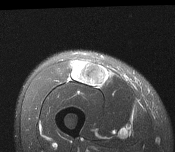
MRI of an extremity soft-tissue mass, one axial slice. Position 54 of 116 along the scan axis. T2-weighted fat-saturated. MR volume resampled by the dataset authors to the PET/CT grid (not the native acquisition matrix). 3.27 mm slice thickness. 175 × 152 image matrix, field of view 171 × 148 mm. Male patient. From the clinical record (not read from this slice): histological type: pleiomorphic leiomyosarcoma; grade: intermediate; site of the primary tumour: right thigh.
Outlined on this slice (expert contour drawn on MRI and transferred to this co-registered scan by the dataset authors):
- gross tumour volume including surrounding oedema: bounding box (x1, y1, x2, y2) in pixels: (70, 61, 109, 87)